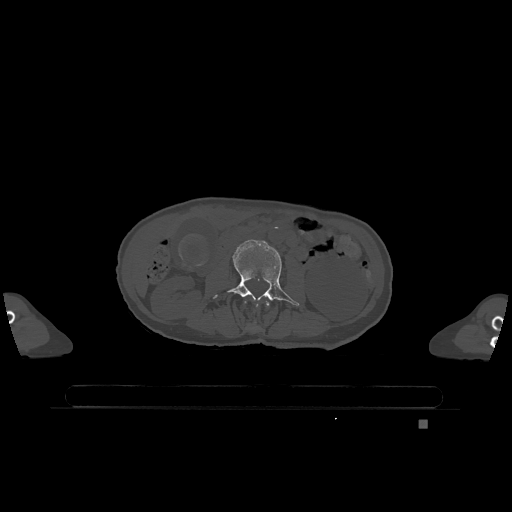
CT including the spine, one axial slice; position 361 of 1317 along the scan axis; bone window (W 1800 / L 400 HU); 0.5 mm slice thickness; 512 × 512 image matrix, field of view 500 × 500 mm. Patient: female, 74 years. From the clinical record (not read from this slice): primary cancer: lung; vertebrae with lytic lesions (as recorded): T1, T4, T5, T6, L4, L5.
Outlined on this slice (semi-automatic segmentation, software-assisted and operator-edited):
- L2 vertebra: box from (x=244, y=301) to (x=270, y=306) px
- L3 vertebra: (x=213, y=240)–(x=299, y=306)